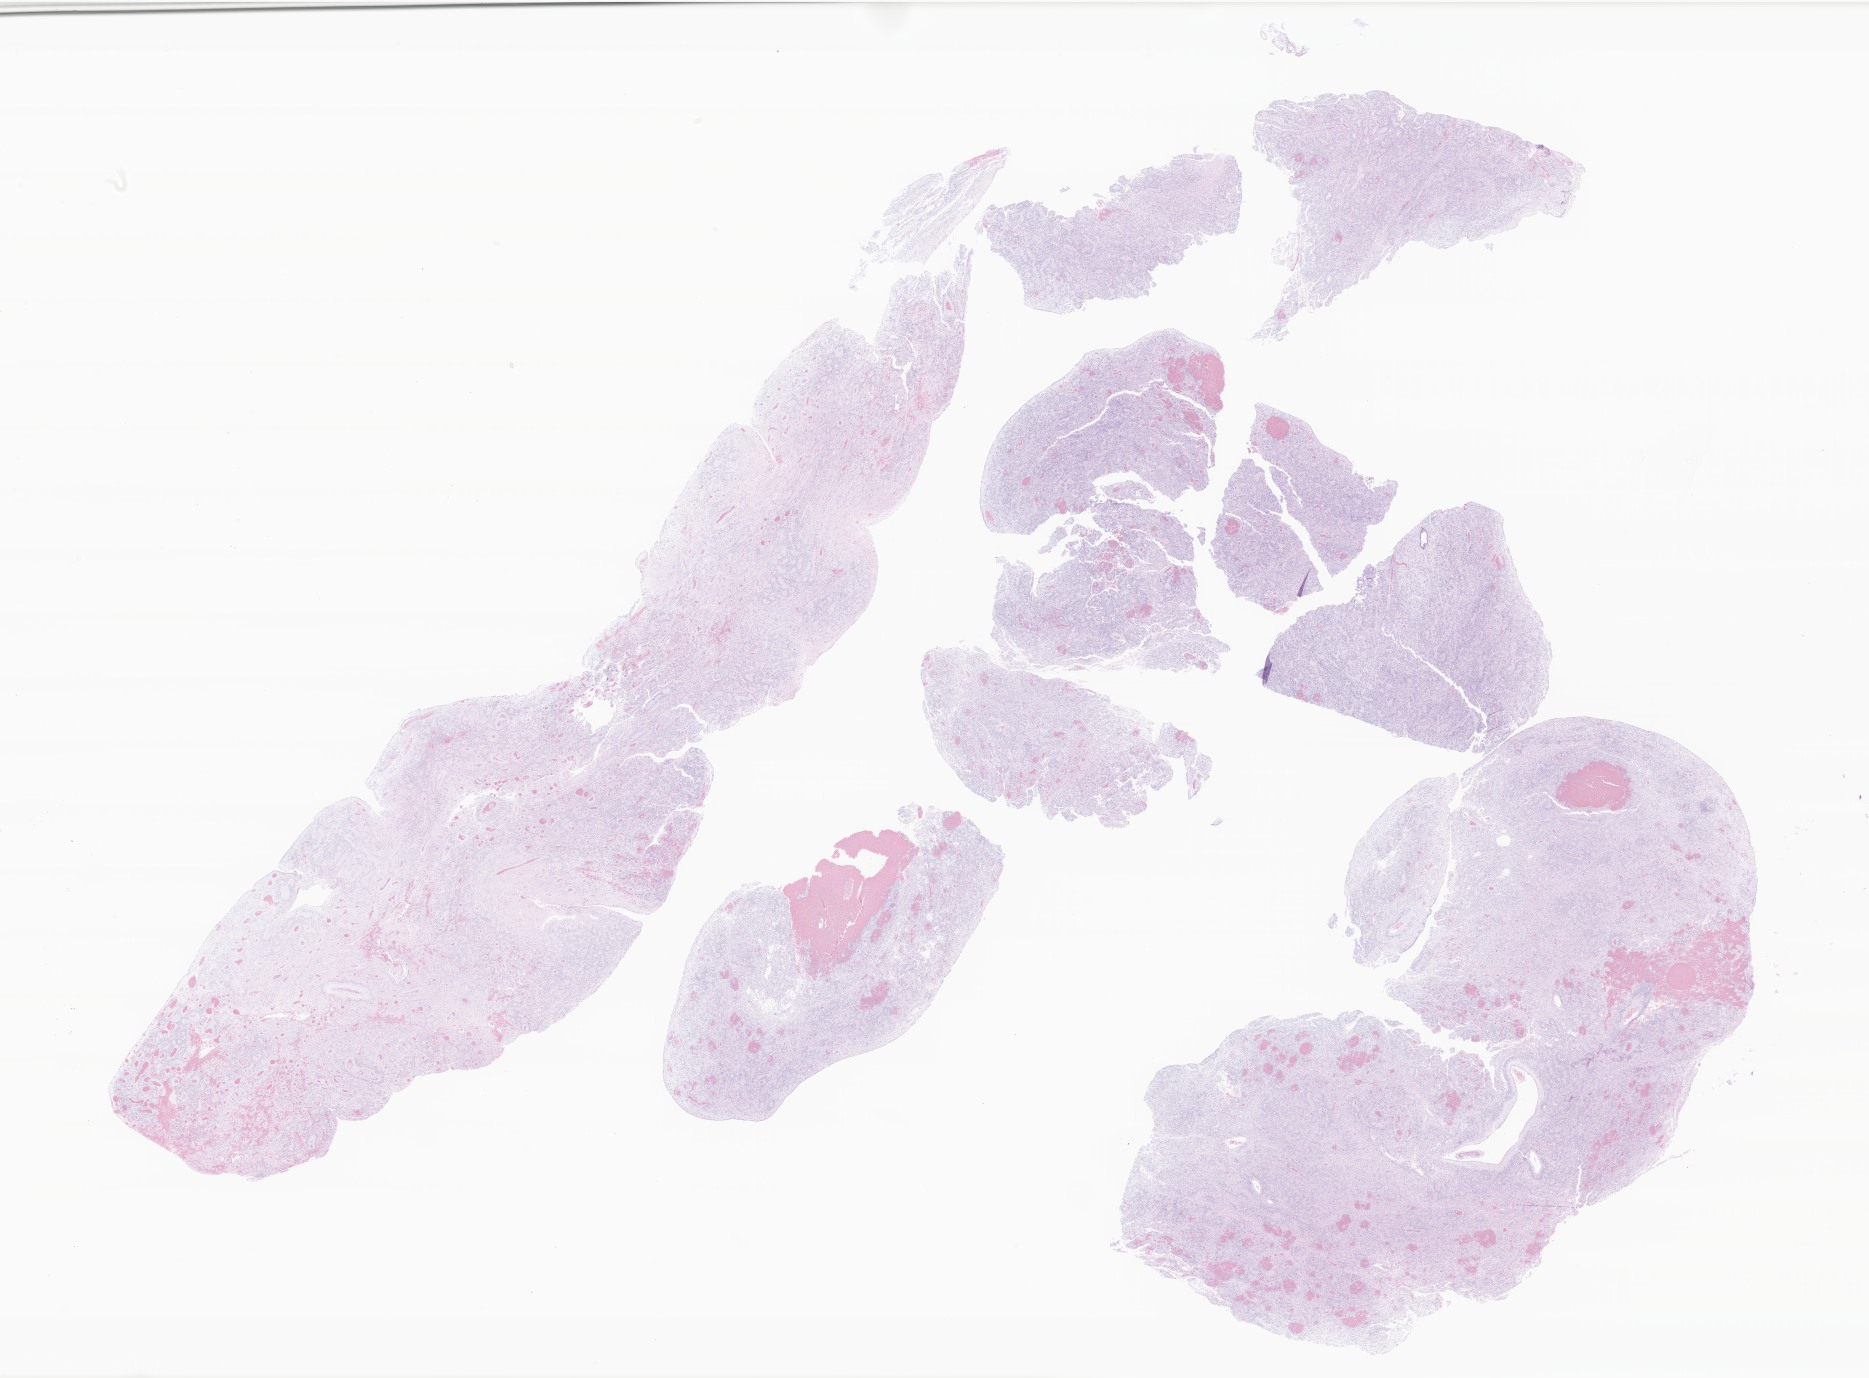
Digitized hematoxylin and eosin (H&E)-stained section of tumor tissue from the brain — shown as a low-resolution overview of the whole scanned area (about 31.5 x 23.2 mm); formalin-fixed paraffin-embedded section. Patient: female, age 877 days (about 2.4 years).
Recorded diagnosis: Ependymoma, NOS.